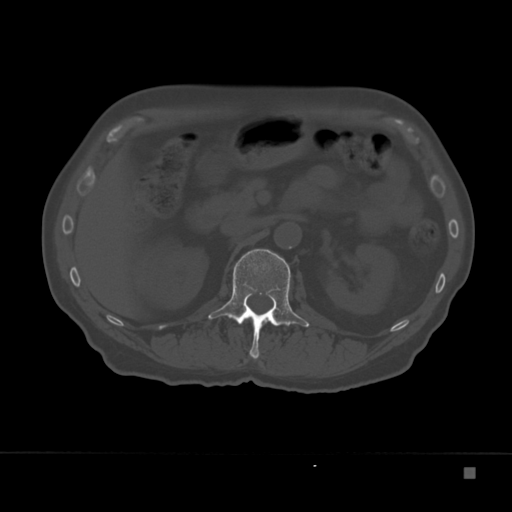
CT including the spine, one axial slice. Slice 112 of 332 in the series (ordered by position). 120 kVp. Bone window (W 1800 / L 400 HU). 1.5 mm slice thickness. 512 × 512 image matrix. Patient: male, 72 years. From the clinical record (not read from this slice): primary cancer: skeletal.
Annotated regions visible in this slice (semi-automatic segmentation, software-assisted and operator-edited):
- L1 vertebra: bounding box <208,249,310,359> (left, top, right, bottom; pixels)